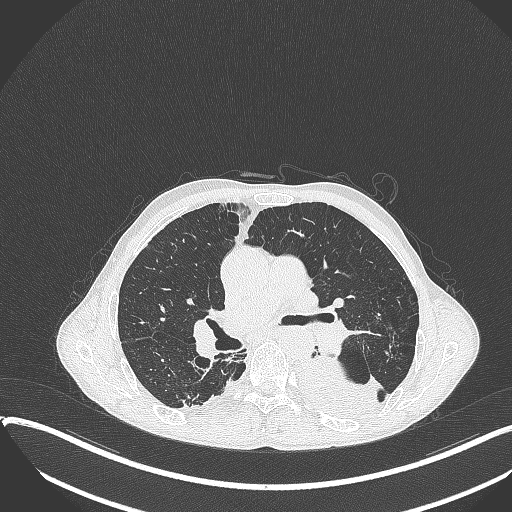
Chest CT, one axial slice; position 224 of 401 along the scan axis; lung window (W 1500 / L -600 HU); 1 mm slice thickness; 512 × 512 image matrix. Male patient, age 57 years. Case-level facts recorded for this patient, not image findings: clinical TNM (as recorded): T4 N0 M0.
Annotated regions visible in this slice (bounding box drawn by a radiologist):
- lung tumour (recorded histology: squamous cell carcinoma): bounding box [x1, y1, x2, y2] px = [291, 353, 390, 421]